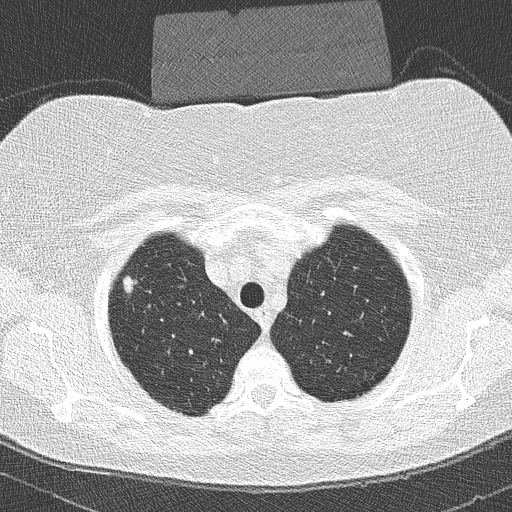
Low-dose screening chest CT, axial slice, second screening round (one year after baseline), lung window (W 1500 / L -600 HU), lung (sharp) reconstruction kernel (B50f), 512 × 512 image matrix, field of view 320 × 320 mm. Female participant, aged 58 years at enrolment.
- Lesion marked by an expert reader, bounding box [x1, y1, x2, y2] px = [111, 270, 150, 306].
- The screening reader recorded 2 non-calcified nodules or masses ≥4 mm on this exam; which of them this box marks is not recorded.
- Official screen result: positive, other.
- Later outcome: lung cancer diagnosed 447 days after this screen — bronchiolo-alveolar adenocarcinoma, NOS, right upper lobe, well differentiated (G1), stage IA (AJCC 6th edition), 9 mm at pathology.